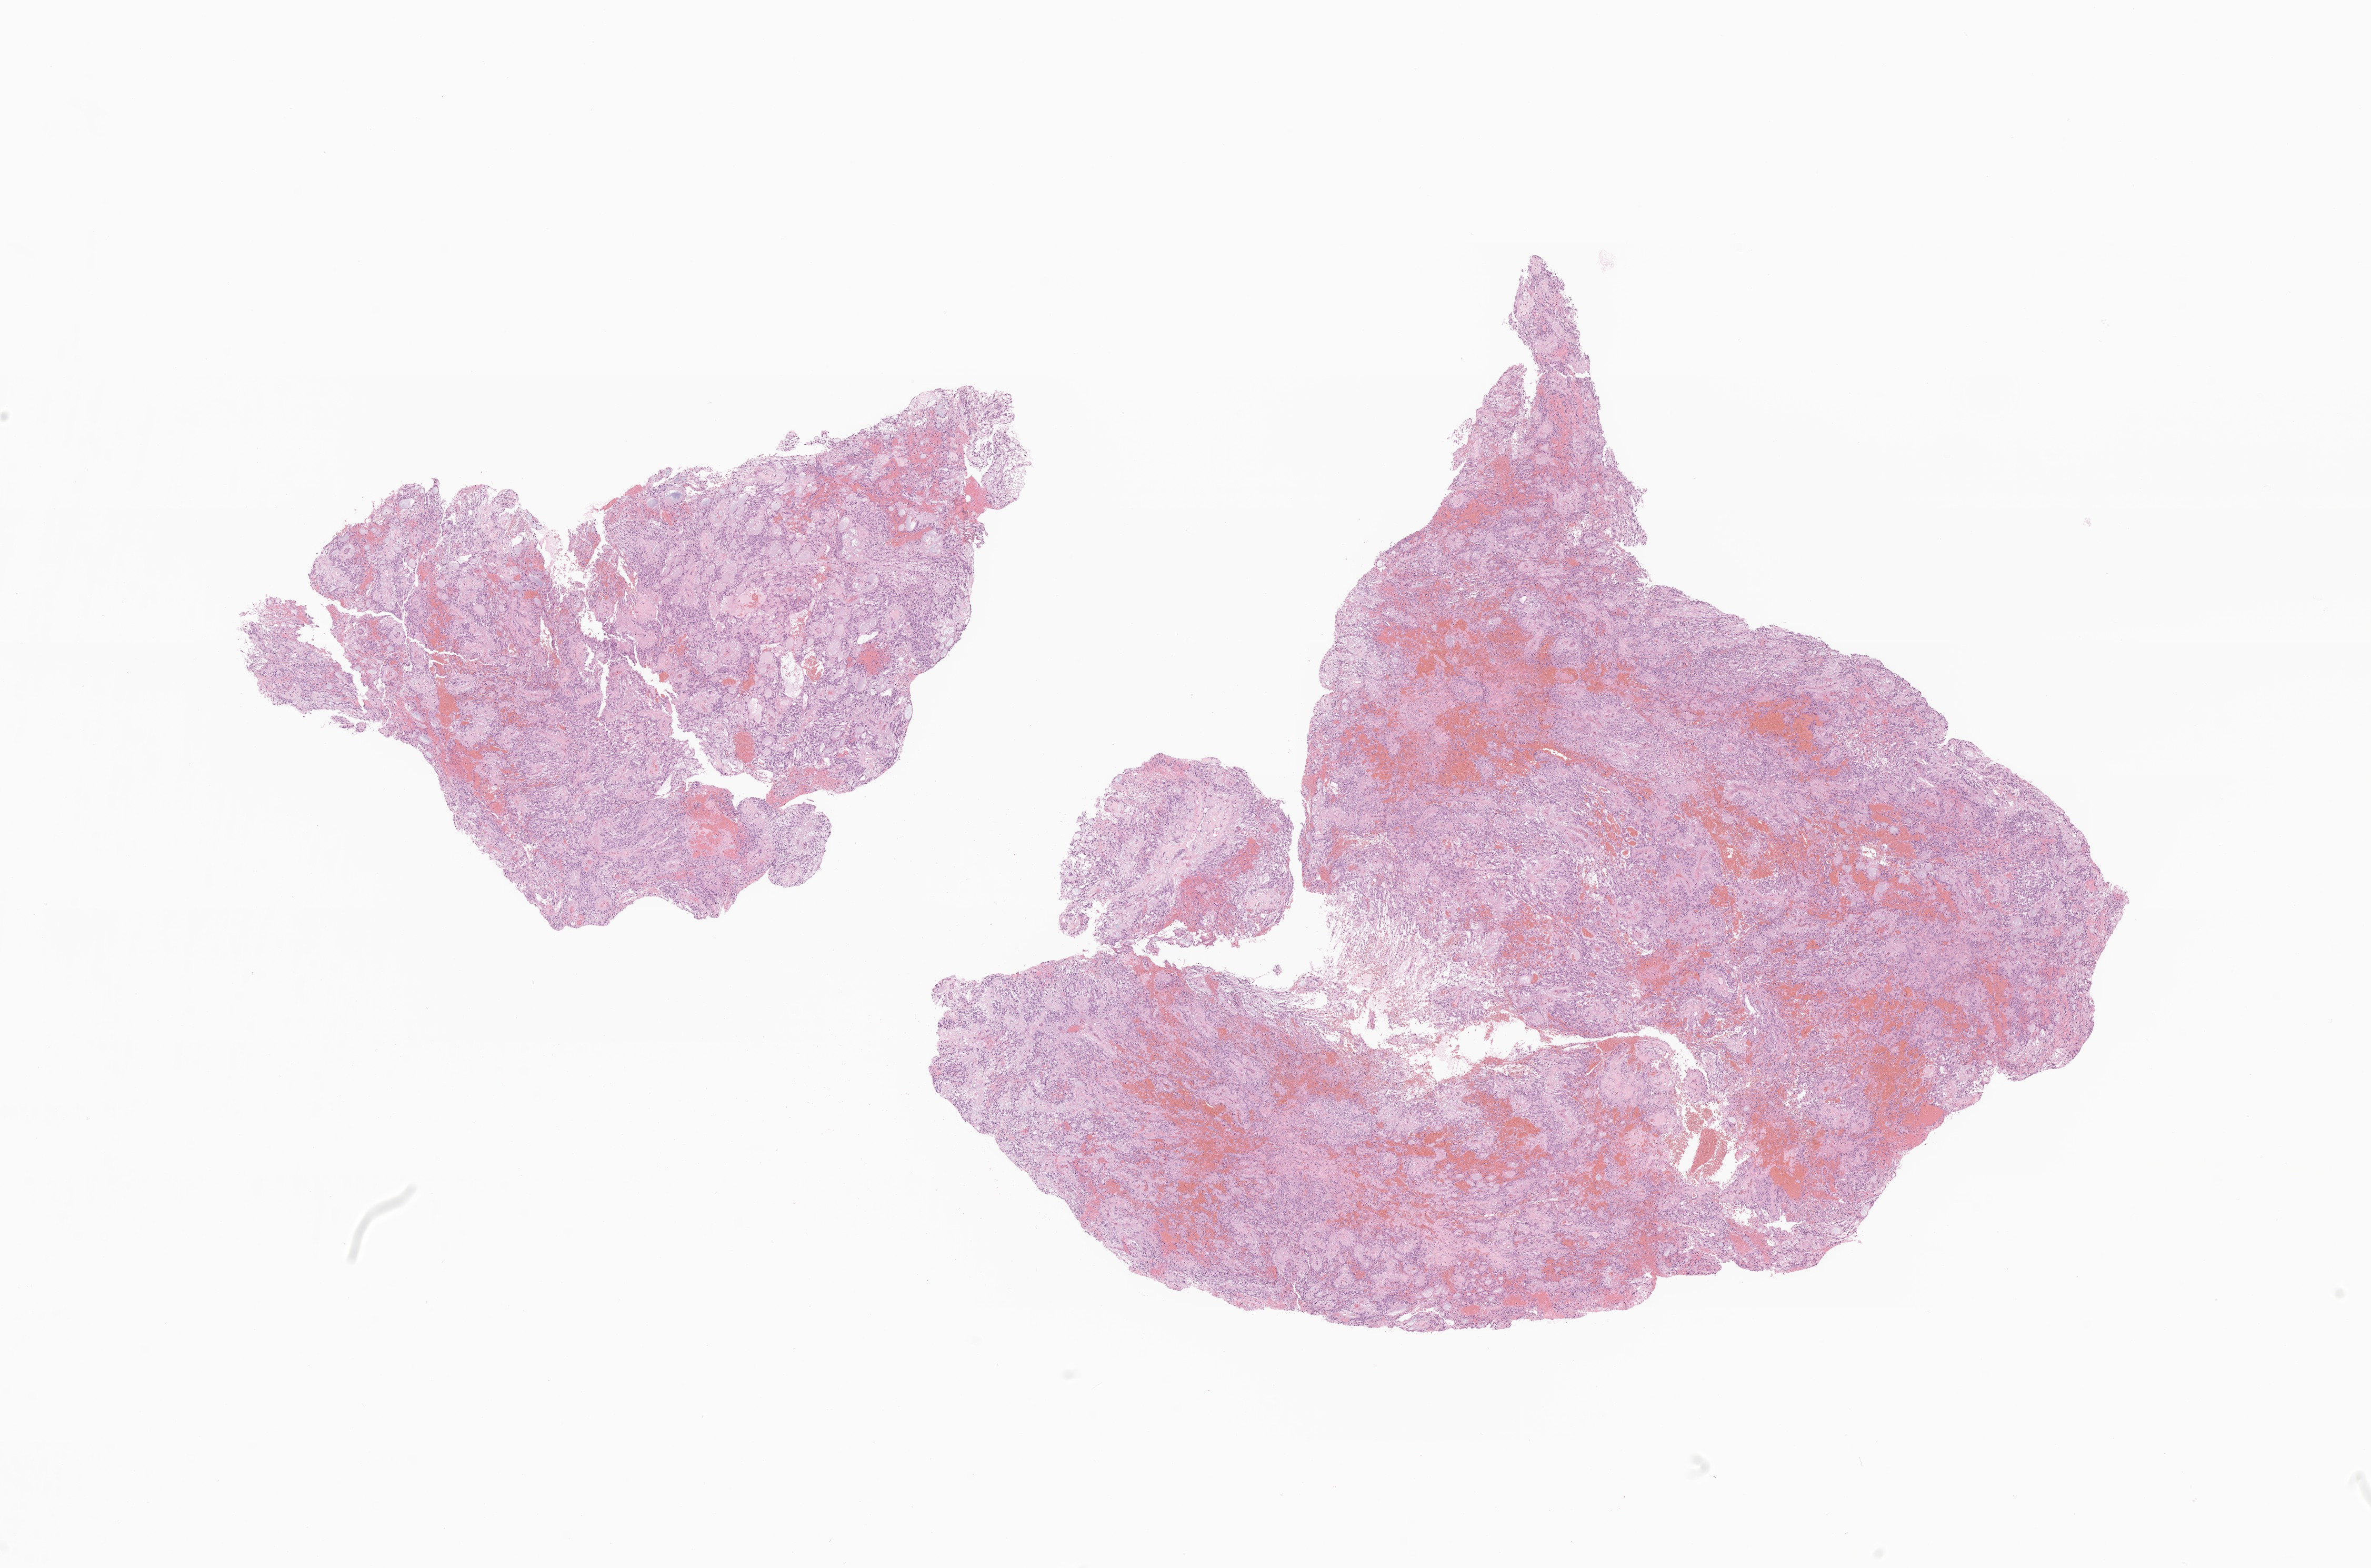
Digitized H&E-stained section of tumor tissue from the spinal cord, whole scanned area (about 19.0 x 12.6 mm) shown as a low-resolution overview. FFPE section. Female patient, age 66 months (5 years 6 months).
Diagnosis (ICD-O-3 morphology term): Myxopapillary ependymoma.